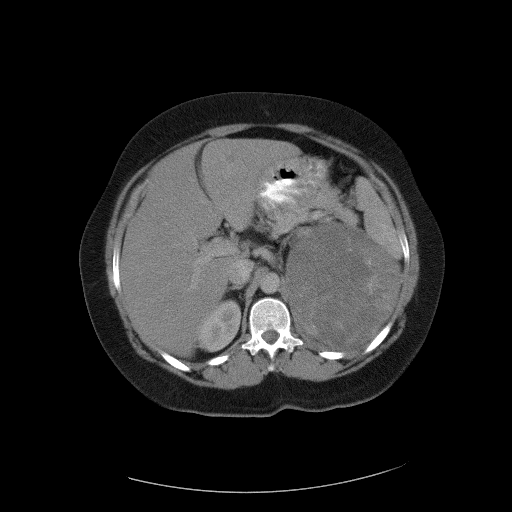
Contrast-enhanced abdominal CT, one axial slice. Position 70 of 90 along the scan axis. Reconstruction kernel FC01. 120 kVp. Intravenous contrast given. Soft-tissue window (W 400 / L 40 HU). 512 × 512 image matrix. Female patient, age 55 years. Case-level facts recorded for this patient, not image findings: diagnosis: adrenocortical carcinoma; tumour side: left adrenal; tumour size at pathology: 22 cm.
Structures marked on this image (semi-automatically segmented with operator editing):
- mass: bounding box <290,228,397,347> (left, top, right, bottom; pixels)